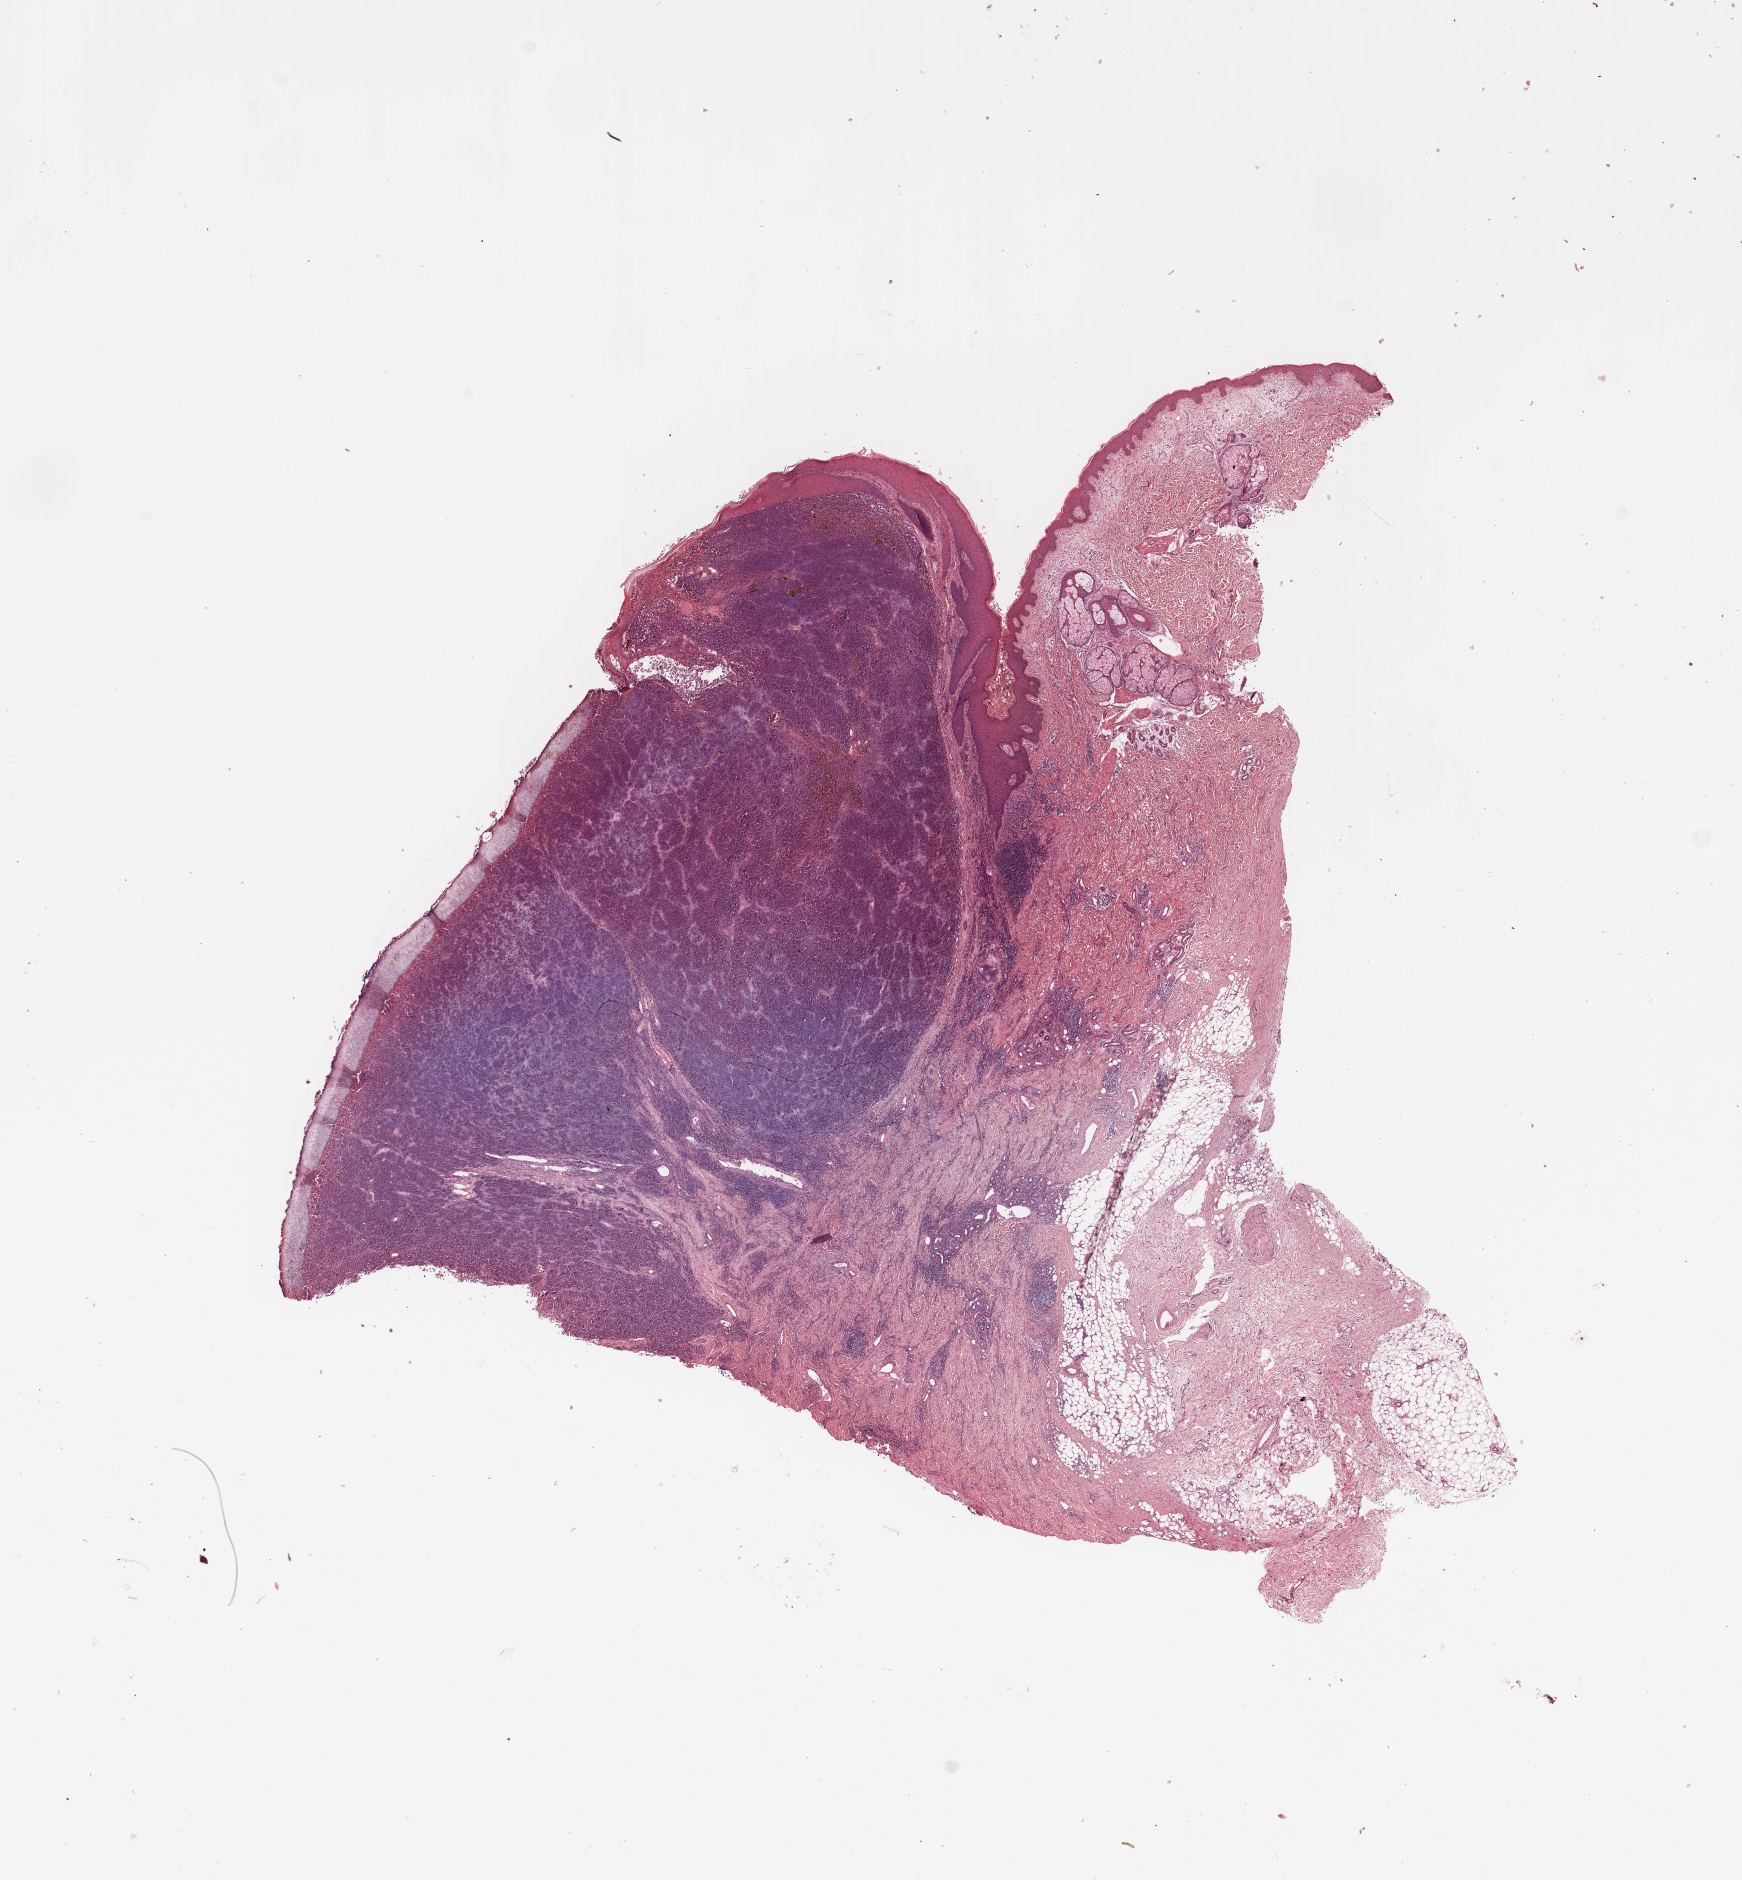
Digitized Hematoxylin and eosin (H&E) stained tissue section (whole slide) — low-resolution overview of the scanned area, about 13.8 x 14.9 mm (acquisition: 20x scan), melanoma tumour tissue; sampled site not recorded. Patient: male, age 59 years.
AJCC pathologic stage: IIC. Histologic diagnosis: Malignant melanoma, NOS. Primary tumour site (as recorded): extremities.